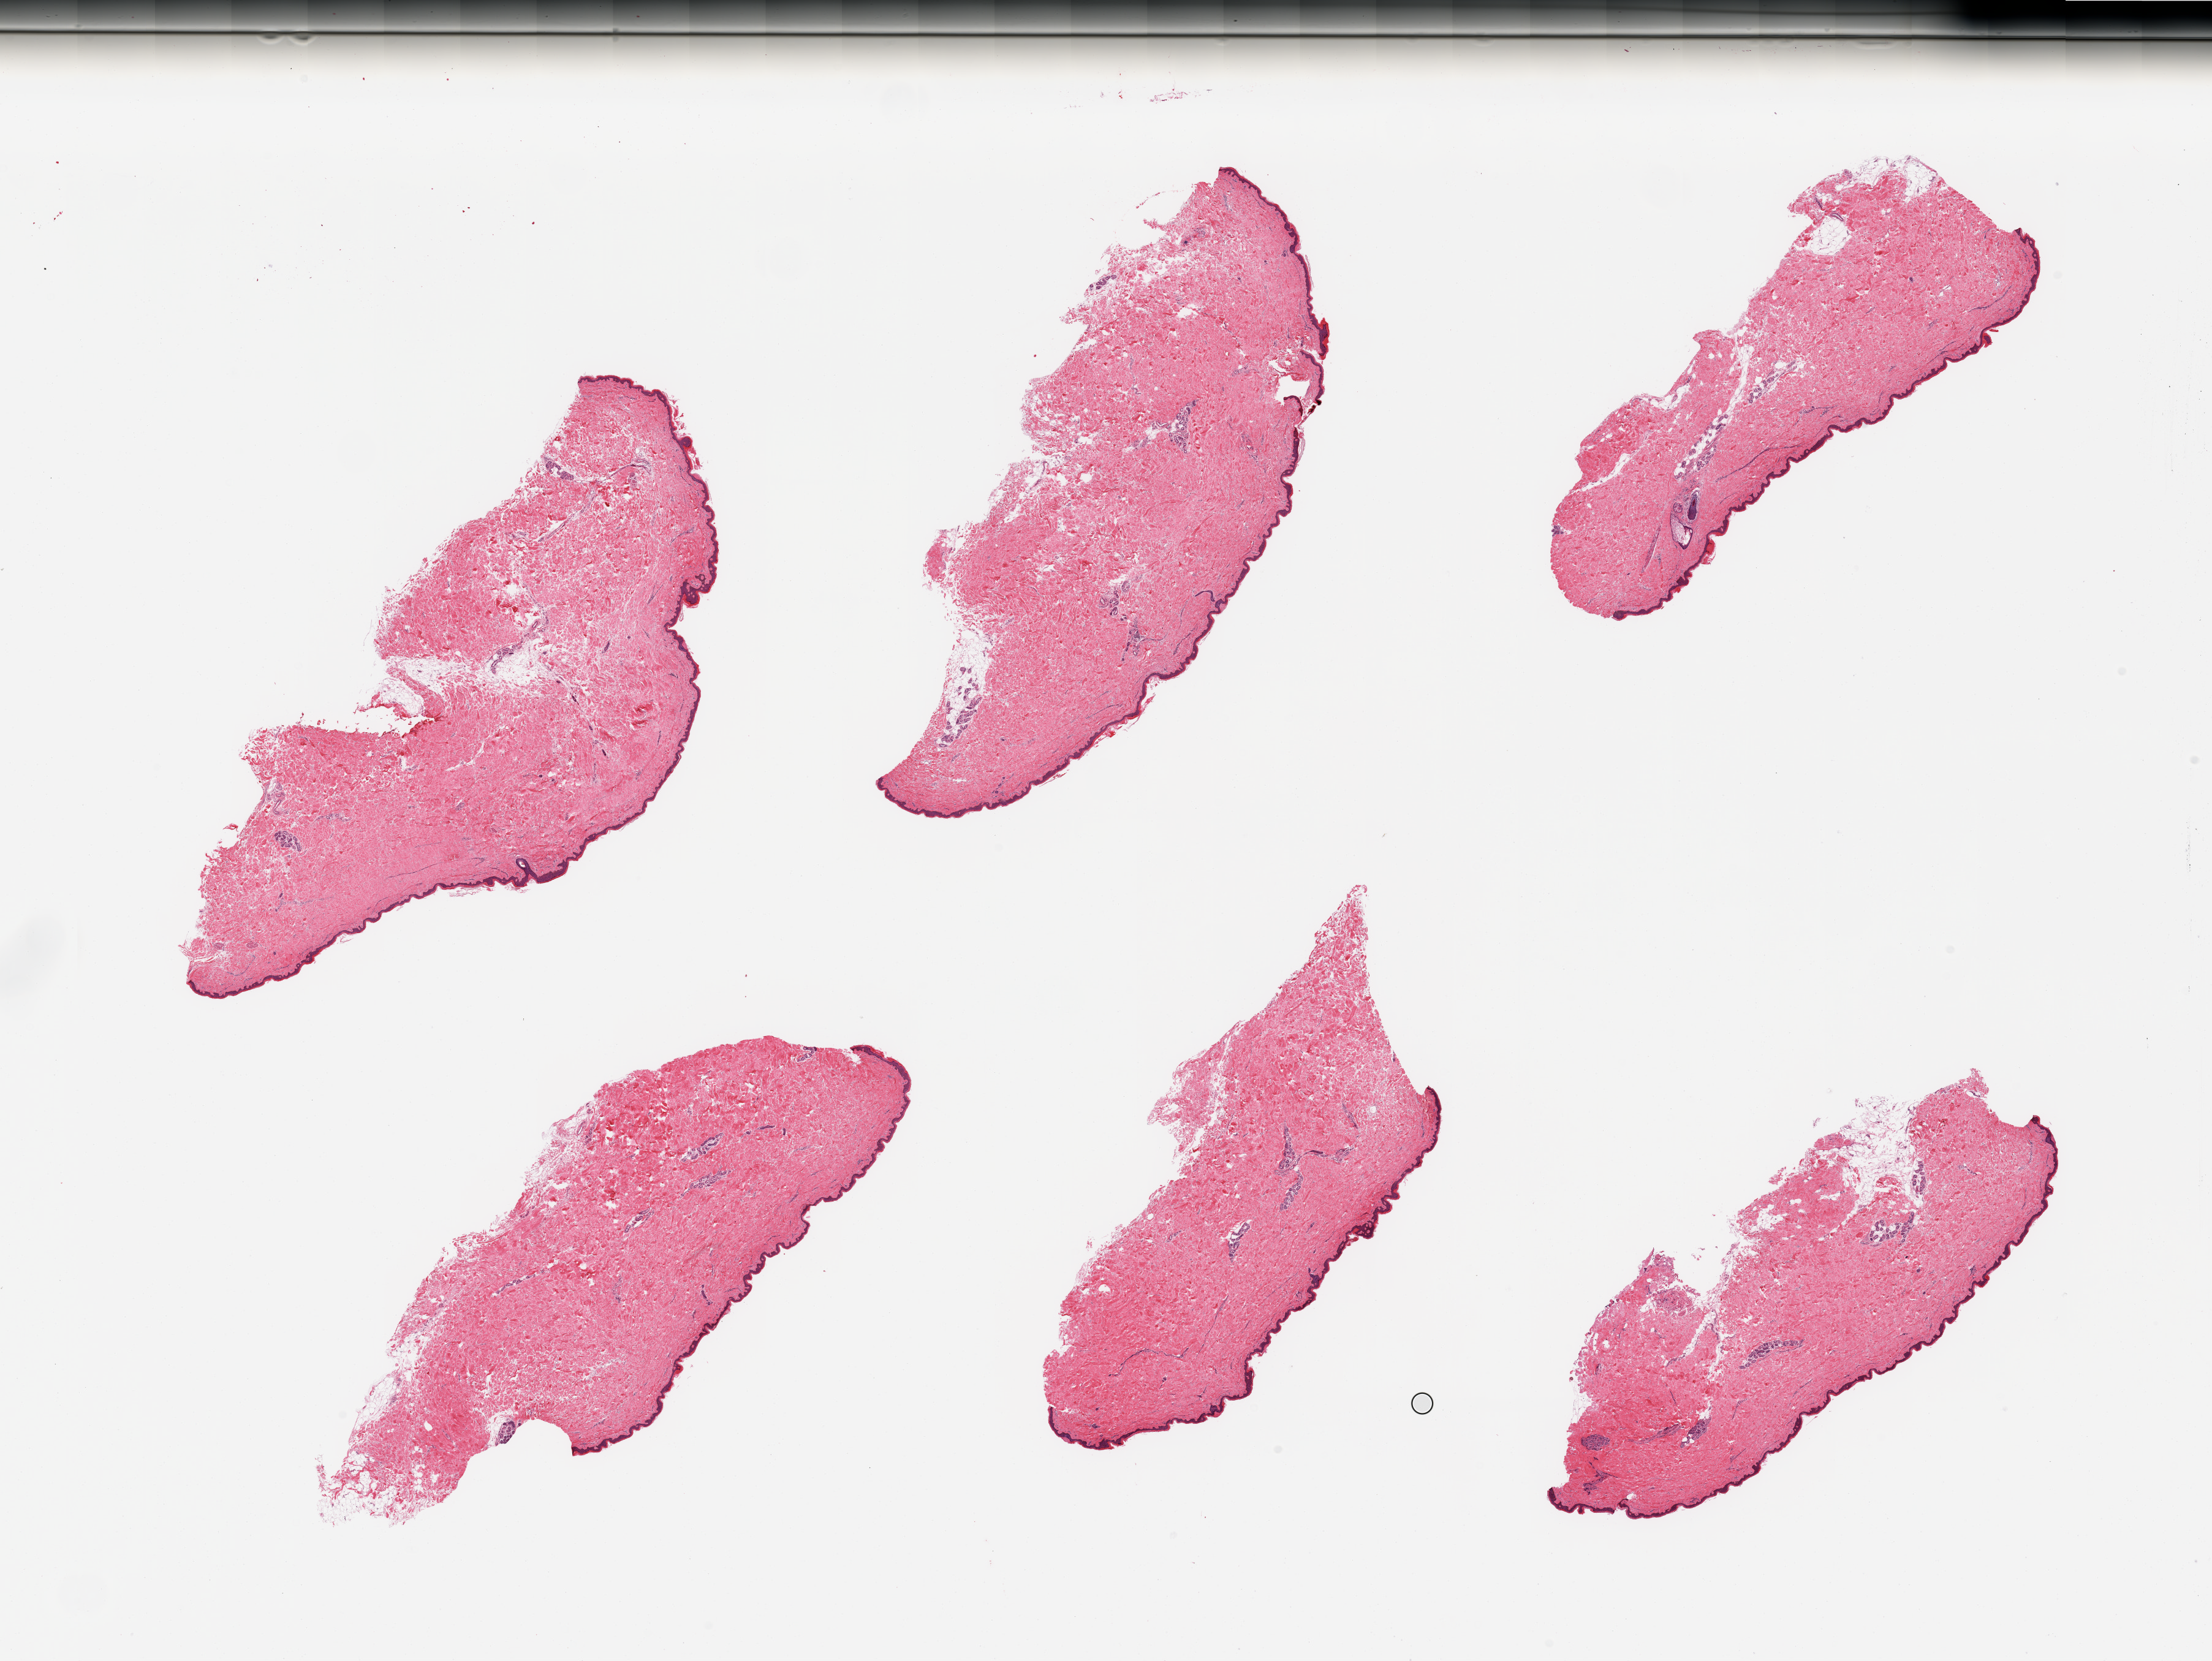
Whole-slide image, H&E stain, a low-resolution overview of the entire scanned area, about 28.5 x 21.4 mm, PAXgene-fixed, paraffin-embedded tissue, section of skin of suprapubic region (target tissue), donor tissue sample. Donor: female.
Review note (as recorded): 6 pieces; 5% dermal fat; well trimmed.